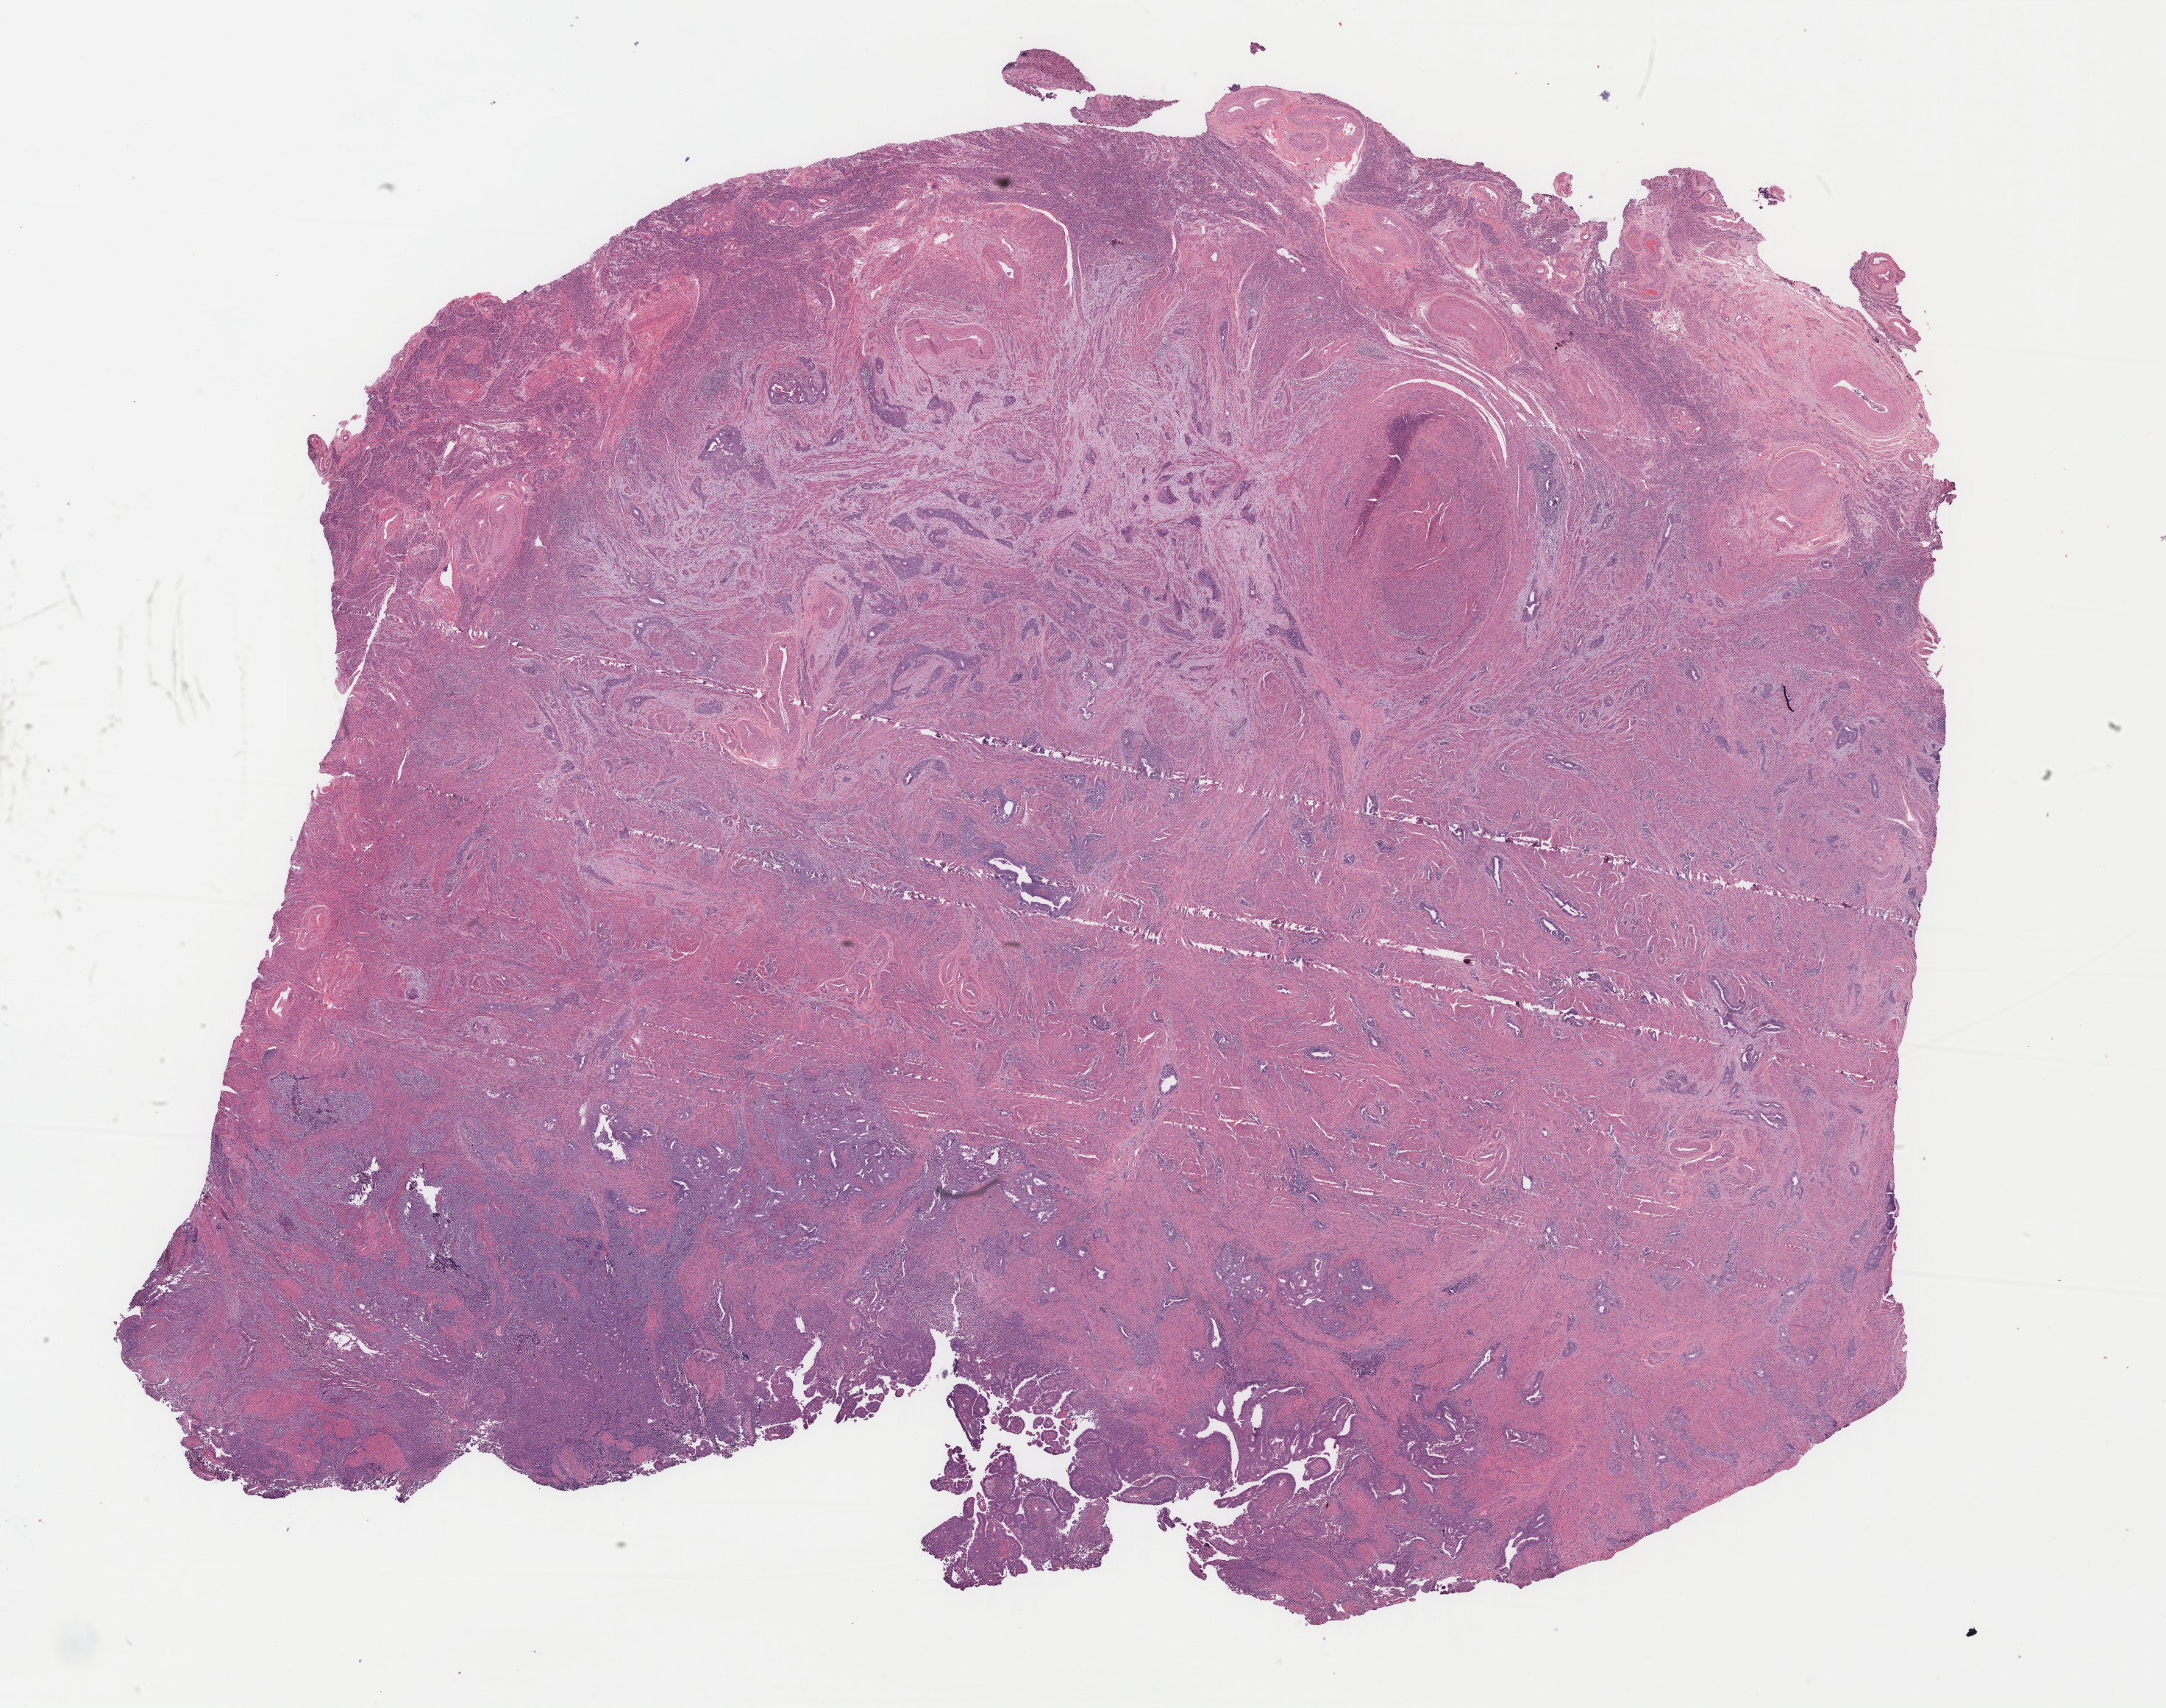
H&E-stained whole-slide image — a low-resolution overview of the entire scanned area, about 23.4 x 18.4 mm. Formalin-fixed paraffin-embedded (FFPE) diagnostic section. Primary tumour sample from the uterus. Female, age 65 years at initial diagnosis. Histologic grade: G3 (poorly differentiated).
* diagnosis: Serous cystadenocarcinoma, NOS (endometrium)
* lymph nodes positive (case pathology): 0 of 11 examined
* FIGO stage: IC